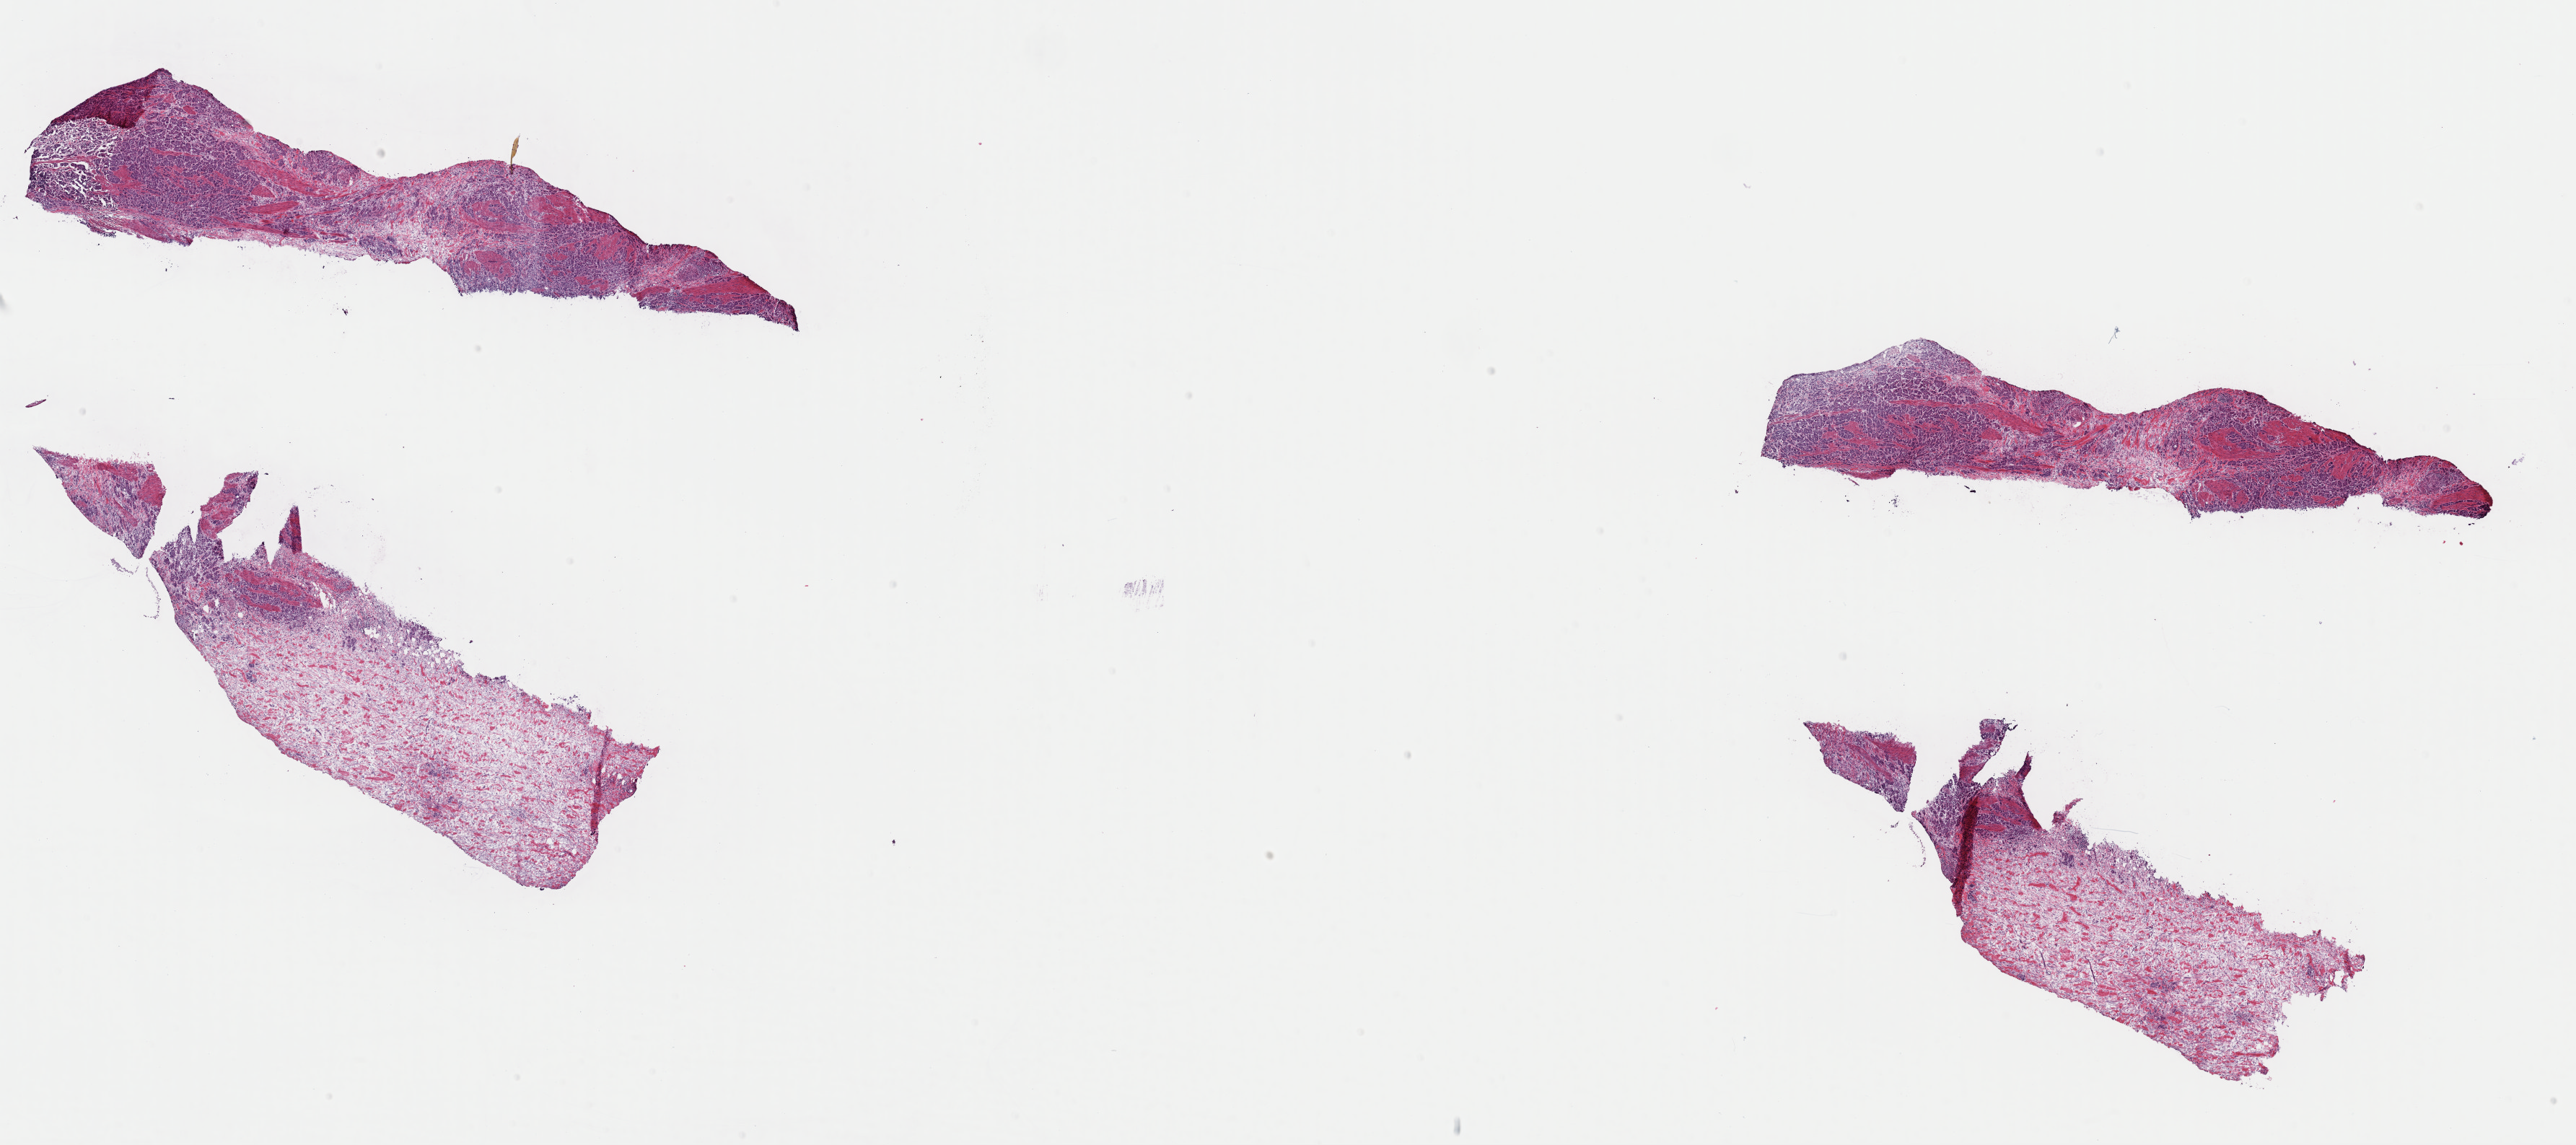
H&E whole-slide image, shown as a low-resolution overview of the whole scanned area (about 28.2 x 12.5 mm); frozen section; sample: primary tumour, bladder. Patient: male, age at initial diagnosis 68 years. Histologic grade: high grade. Slide review estimates, as recorded: tumour cells 70%, tumour nuclei 70%, normal cells 0%, stromal cells 30%, necrosis 0%. Infiltration values recorded for this section: lymphocyte infiltration 5%, monocyte infiltration 0%, neutrophil infiltration 0%.
- histologic diagnosis: Transitional cell carcinoma (posterior wall of bladder)
- AJCC pathologic stage: IV (7th edition)
- lymph nodes positive (case pathology): 4 of 16 examined